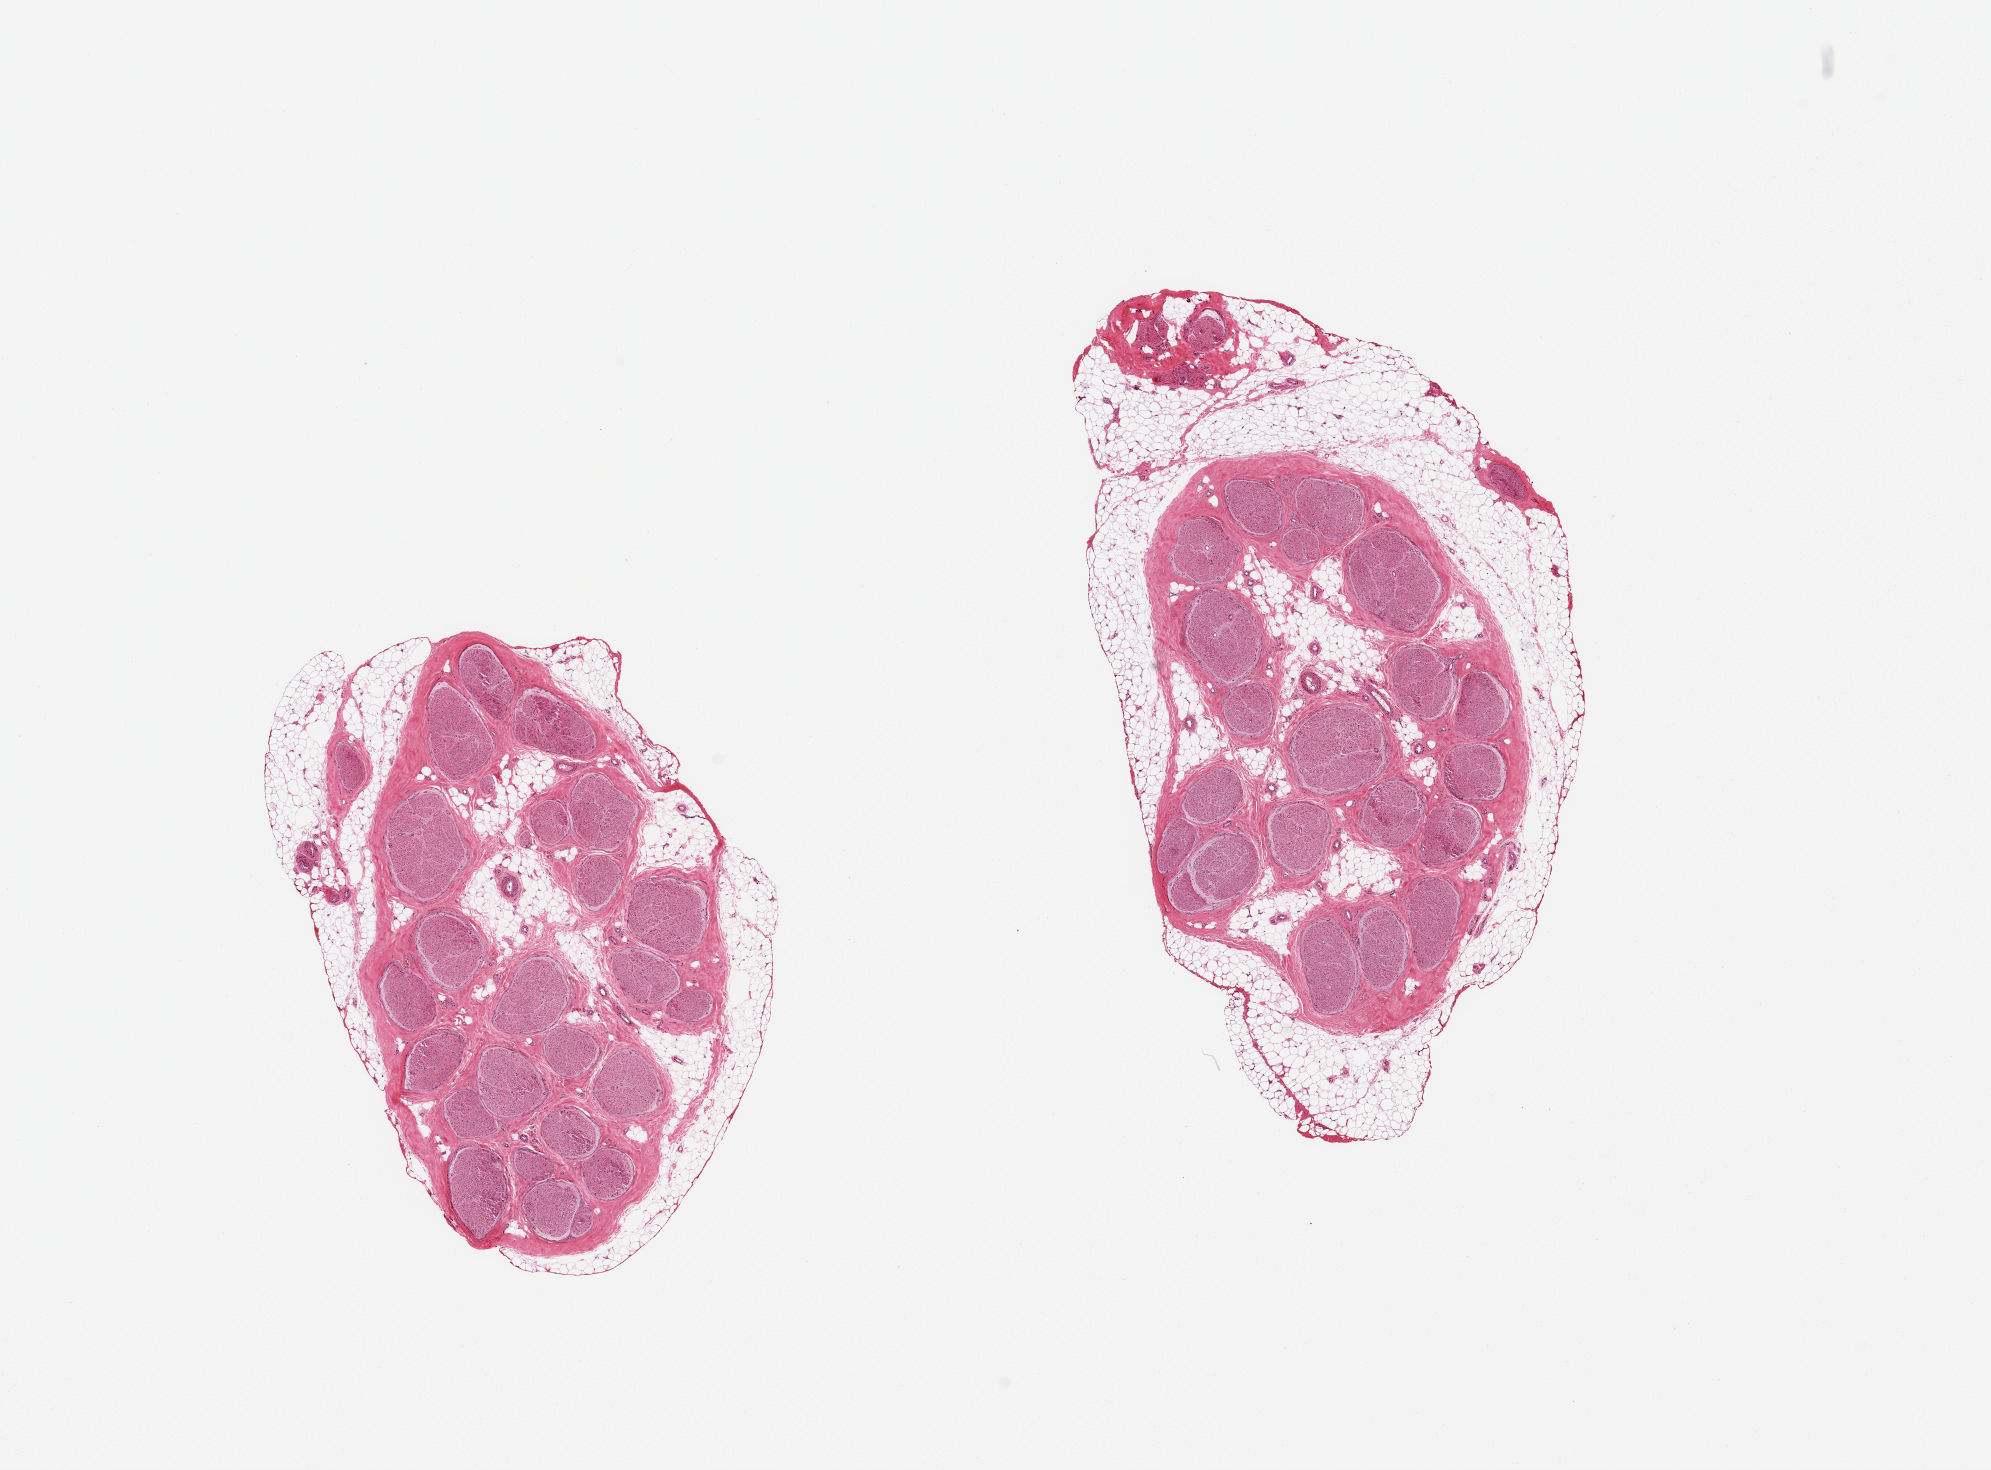
Whole-slide image, H&E stain, whole scanned area (about 15.8 x 11.6 mm) shown as a low-resolution overview, PAXgene-fixed, paraffin-embedded tissue, section of tibial nerve (target tissue), tissue donor sample. Donor: male.
Review note (as recorded): 2 pieces; 20 & 40% internal & external fat content; small arteries have hypertrophic media (?hypertensive effect).